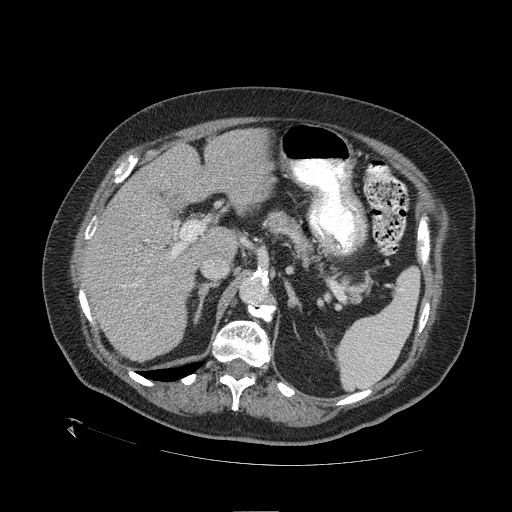
Contrast-enhanced abdominal CT (liver protocol), one axial slice. Slice 69 of 109 in the series (ordered by position). One of 2 acquisitions stored at this slice position. Soft-tissue window (W 400 / L 40 HU). 512 × 512 image matrix, field of view 460 × 460 mm. Case-level facts recorded for this patient, not image findings: diagnosis: hepatocellular carcinoma (patient treated with transarterial chemoembolisation; whether this scan precedes or follows treatment is not stated here); TNM stage (as recorded): Stage-I; Child-Pugh class: A; tumour differentiation: no biopsy; tumour nodularity: uninodular.
Structures marked on this image (semi-automatic segmentation, software-assisted and operator-edited):
- liver parenchyma outside the tumour (the mass and vessels are separate outlines, so this box may not span the whole liver): bounding box (x1, y1, x2, y2) in pixels: (82, 128, 272, 360)
- liver vessels: (86, 219, 184, 287)